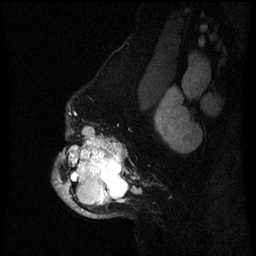
Breast MRI (dynamic contrast-enhanced), one sagittal slice; dynamic contrast-enhanced series, image 2 of 3 at this slice position (ordered by acquisition); 1.5 T; TE 4.2 ms, TR 8 ms; 2 mm slice thickness; 256 × 256 image matrix, field of view 190 × 190 mm. Female patient, age 50 years.
Outlined on this slice (semi-automatically segmented with operator editing):
- analysis volume of interest (the breast-tissue region the enhancement analysis was run in; not a lesion): bounding box (x1, y1, x2, y2) in pixels: (52, 105, 141, 218)
- tumour enhancement mask (voxels above the 70 % enhancement threshold inside the analysis volume of interest): (57, 127, 141, 217)